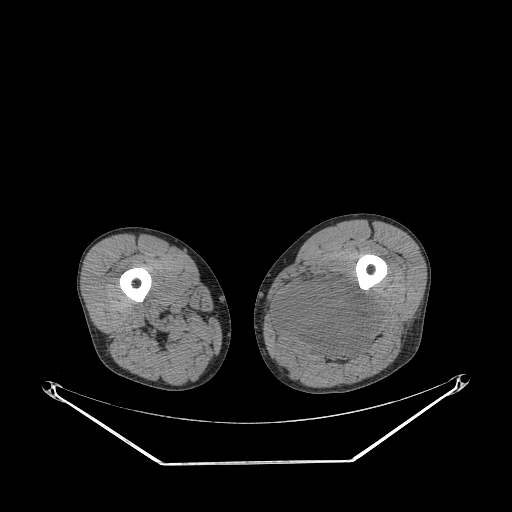
CT of an extremity soft-tissue mass (from a PET/CT study), one axial slice; slice 236 of 267 in the series (ordered by position); reconstruction kernel STANDARD; soft-tissue window (W 400 / L 40 HU); 3.75 mm slice thickness; 512 × 512 image matrix, field of view 500 × 500 mm. Male patient. Case-level facts recorded for this patient, not image findings: histological type: undifferentiated pleomorphic liposarcoma; grade: high; site of the primary tumour: left thigh.
Outlined on this slice (expert contour drawn on MRI and transferred to this co-registered scan by the dataset authors):
- gross tumour volume including surrounding oedema: box from (x=276, y=279) to (x=378, y=362) px
- gross tumour volume (mass): (x=276, y=279)–(x=378, y=359)